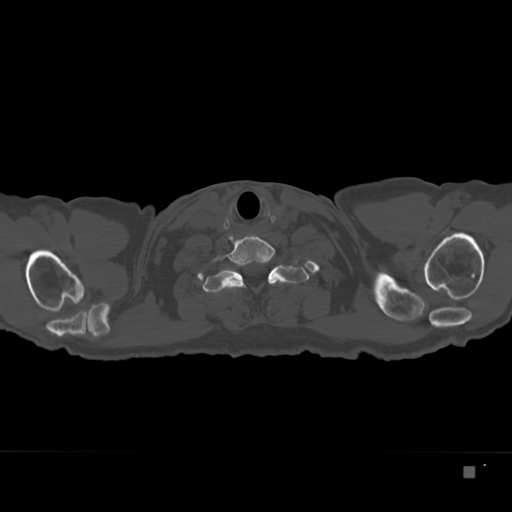
CT including the spine, one axial slice. Slice 322 of 332 in the series (ordered by position). 120 kVp. Bone window (W 1800 / L 400 HU). 512 × 512 image matrix. Patient: male, 72 years. Case-level facts recorded for this patient, not image findings: primary cancer: skeletal.
Annotated regions visible in this slice (semi-automatic segmentation, software-assisted and operator-edited):
- T1 vertebra: box from (x=202, y=258) to (x=309, y=293) px